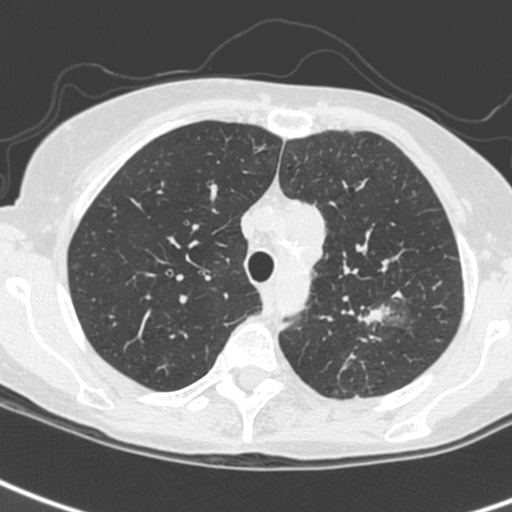
Low-dose screening chest CT, one axial slice. Slice 191 of 242 in the series (ordered by position). 120 kVp. Lung window (W 1500 / L -600 HU). 1.3 mm slice thickness. 512 × 512 image matrix.
Annotated regions visible in this slice (manually delineated by an expert):
- lesion 1 (tumor, upper lobe of left lung): box from (x=363, y=308) to (x=384, y=323) px
- lesion 3 (tumor, upper lobe of left lung): (x=297, y=202)–(x=326, y=266)